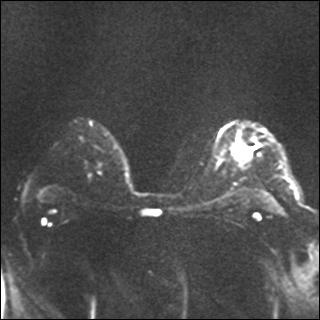
Breast MRI, one axial slice; slice 23 of 35 in the series (ordered by position); diffusion-weighted series; image 2 of 4 stored at this slice position (different b-values; order by instance number); 1.5 T; 4 mm slice thickness; 320 × 320 image matrix. Female patient.
Outlined on this slice (expert manual segmentation):
- tumour on diffusion-weighted imaging: bounding box (x1, y1, x2, y2) in pixels: (239, 144, 251, 158)